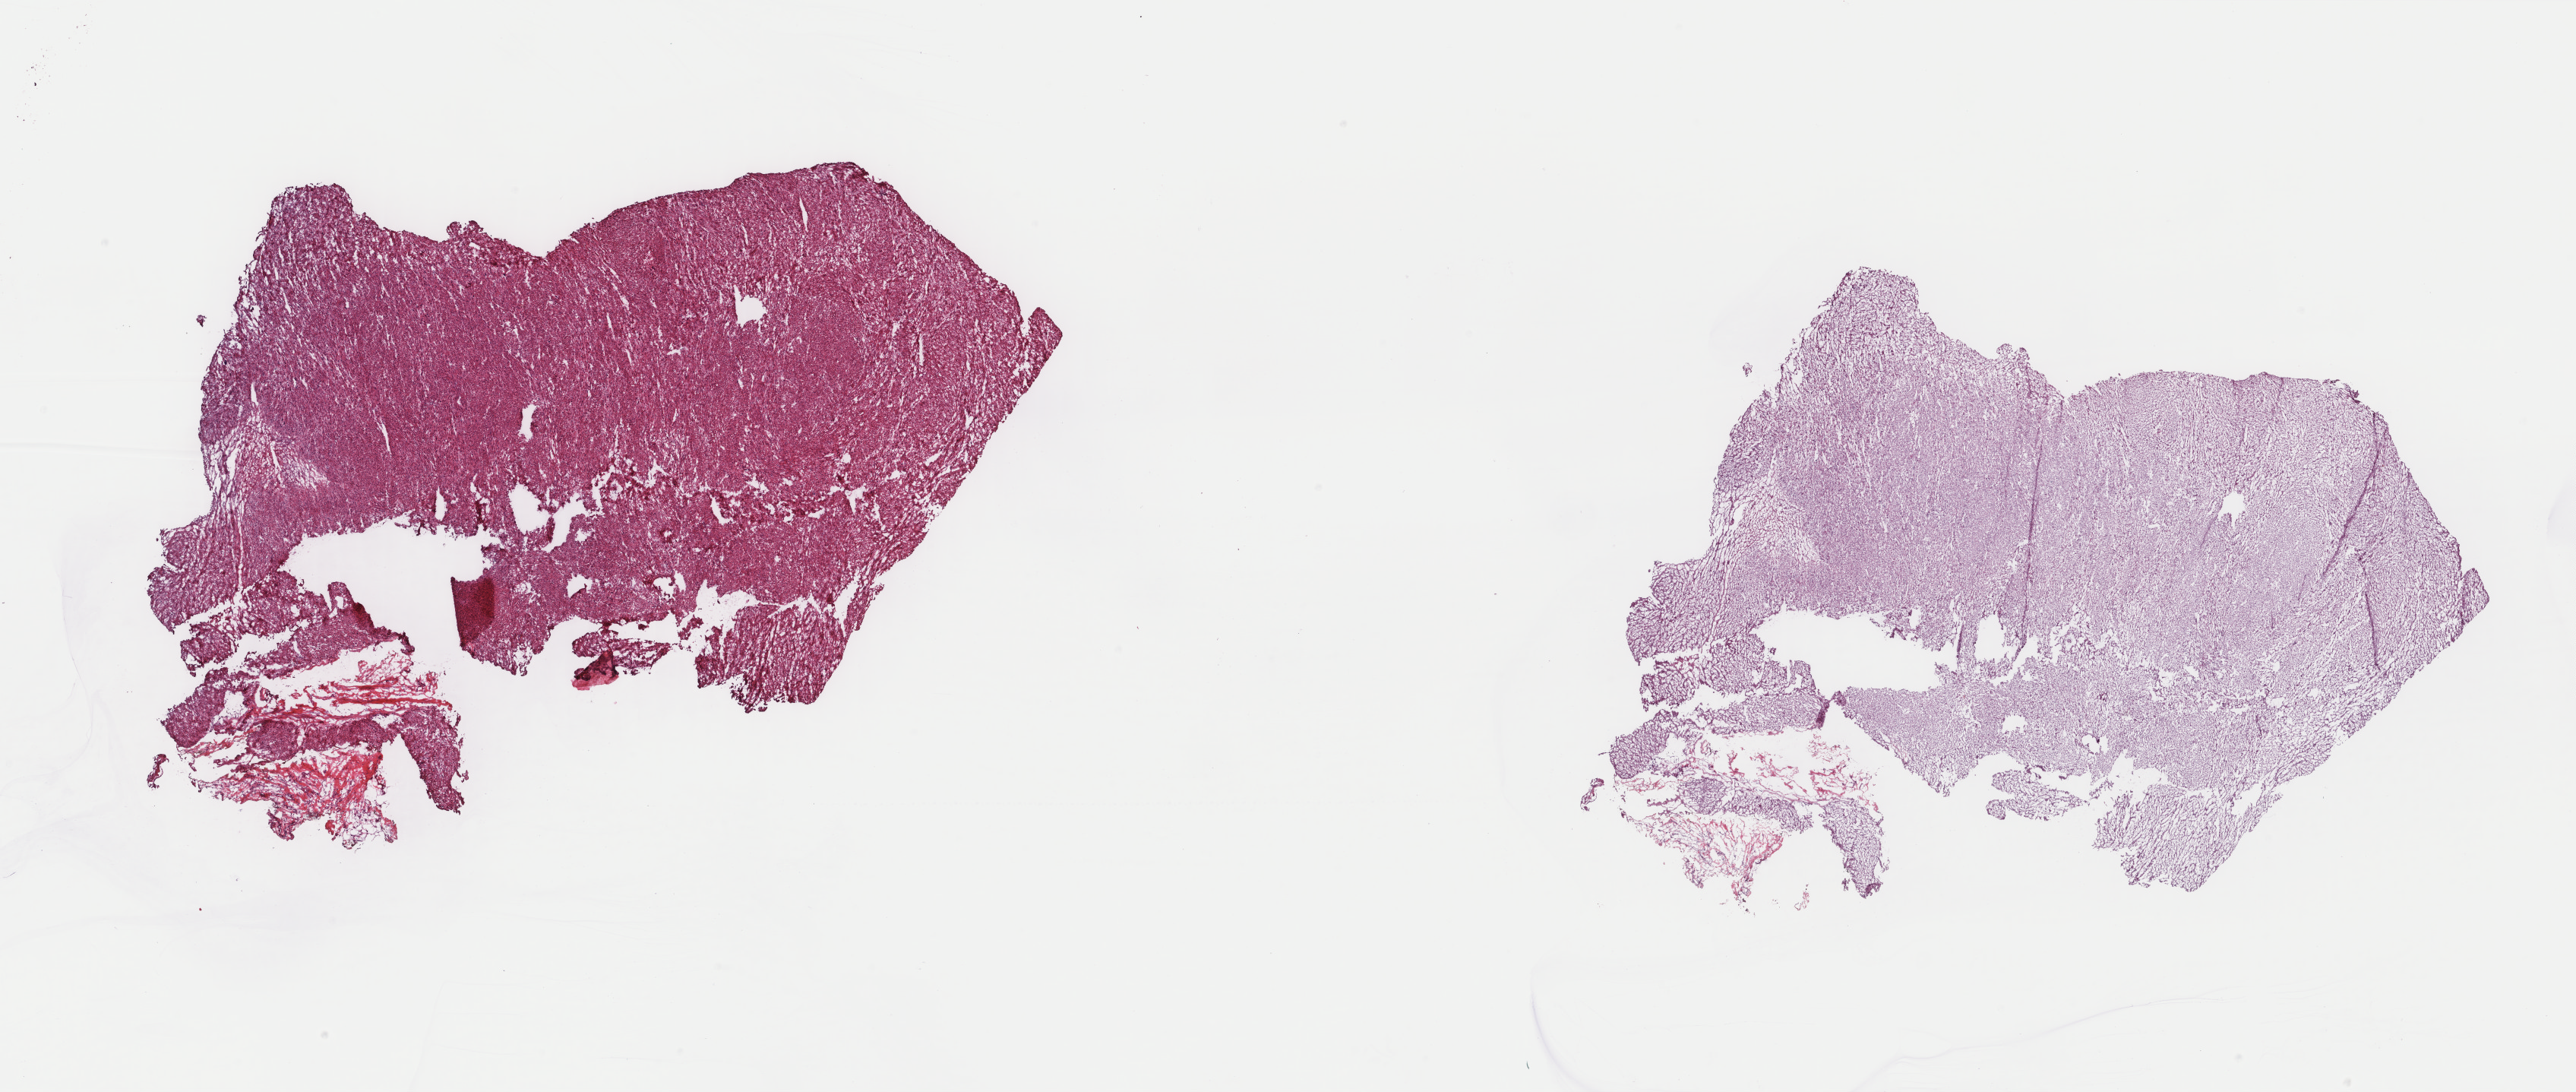
H&E whole-slide image — whole scanned area (about 26.9 x 11.4 mm) shown as a low-resolution overview, frozen section from the top of the tissue portion, recurrent tumour sample from the uterus. Female, age 64 years at initial diagnosis. Pathologist review of this section (percent, as recorded): tumour cells 100%, tumour nuclei 97%, normal cells 0%, stromal cells 0%, necrosis 0%. Infiltration values recorded for this section: lymphocyte infiltration 0%, monocyte infiltration 0%, neutrophil infiltration 0%.
This section: recurrent tumour. Patient diagnosis: Leiomyosarcoma, NOS.